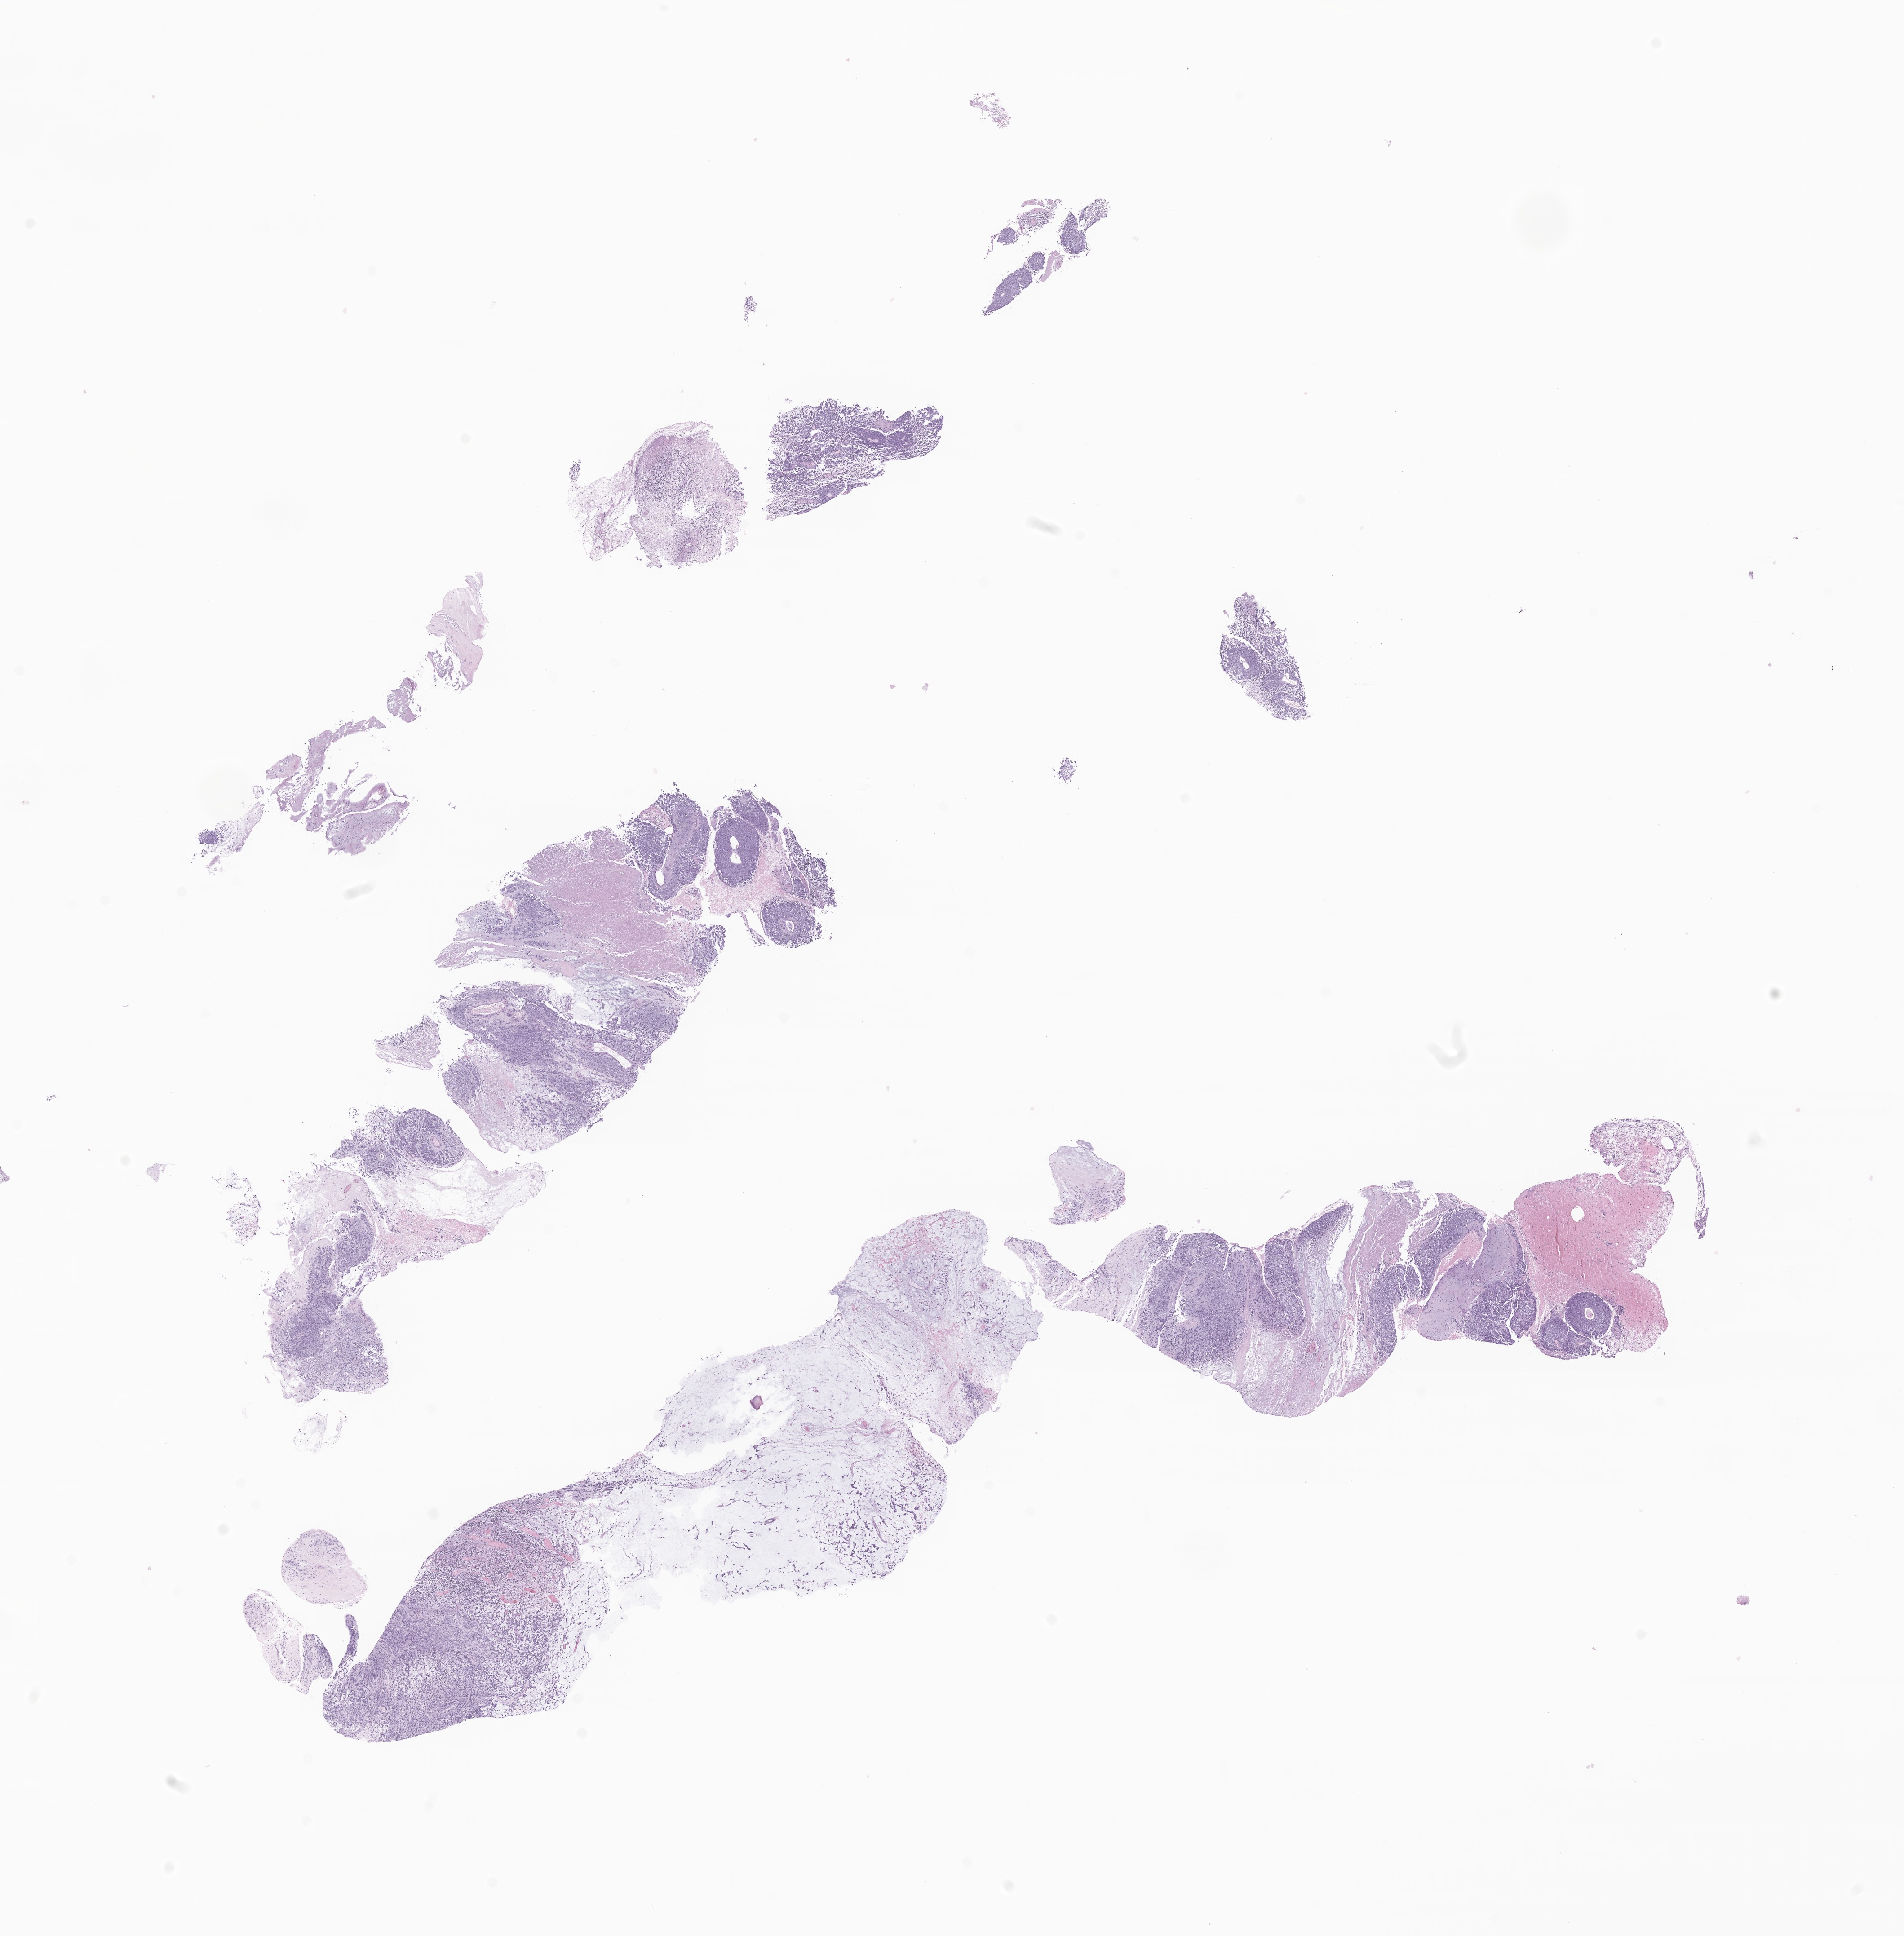
Whole-slide image, H&E stain of tumor tissue from the upper limb lymph node — a low-resolution overview of the entire scanned area, about 17.9 x 18.2 mm; formalin-fixed, paraffin-embedded (FFPE) tissue. Female patient, age 145 months (12 years 1 month).
Diagnosis: Sarcoma, NOS. Tissue or organ of origin (case record): lymph nodes of axilla or arm.